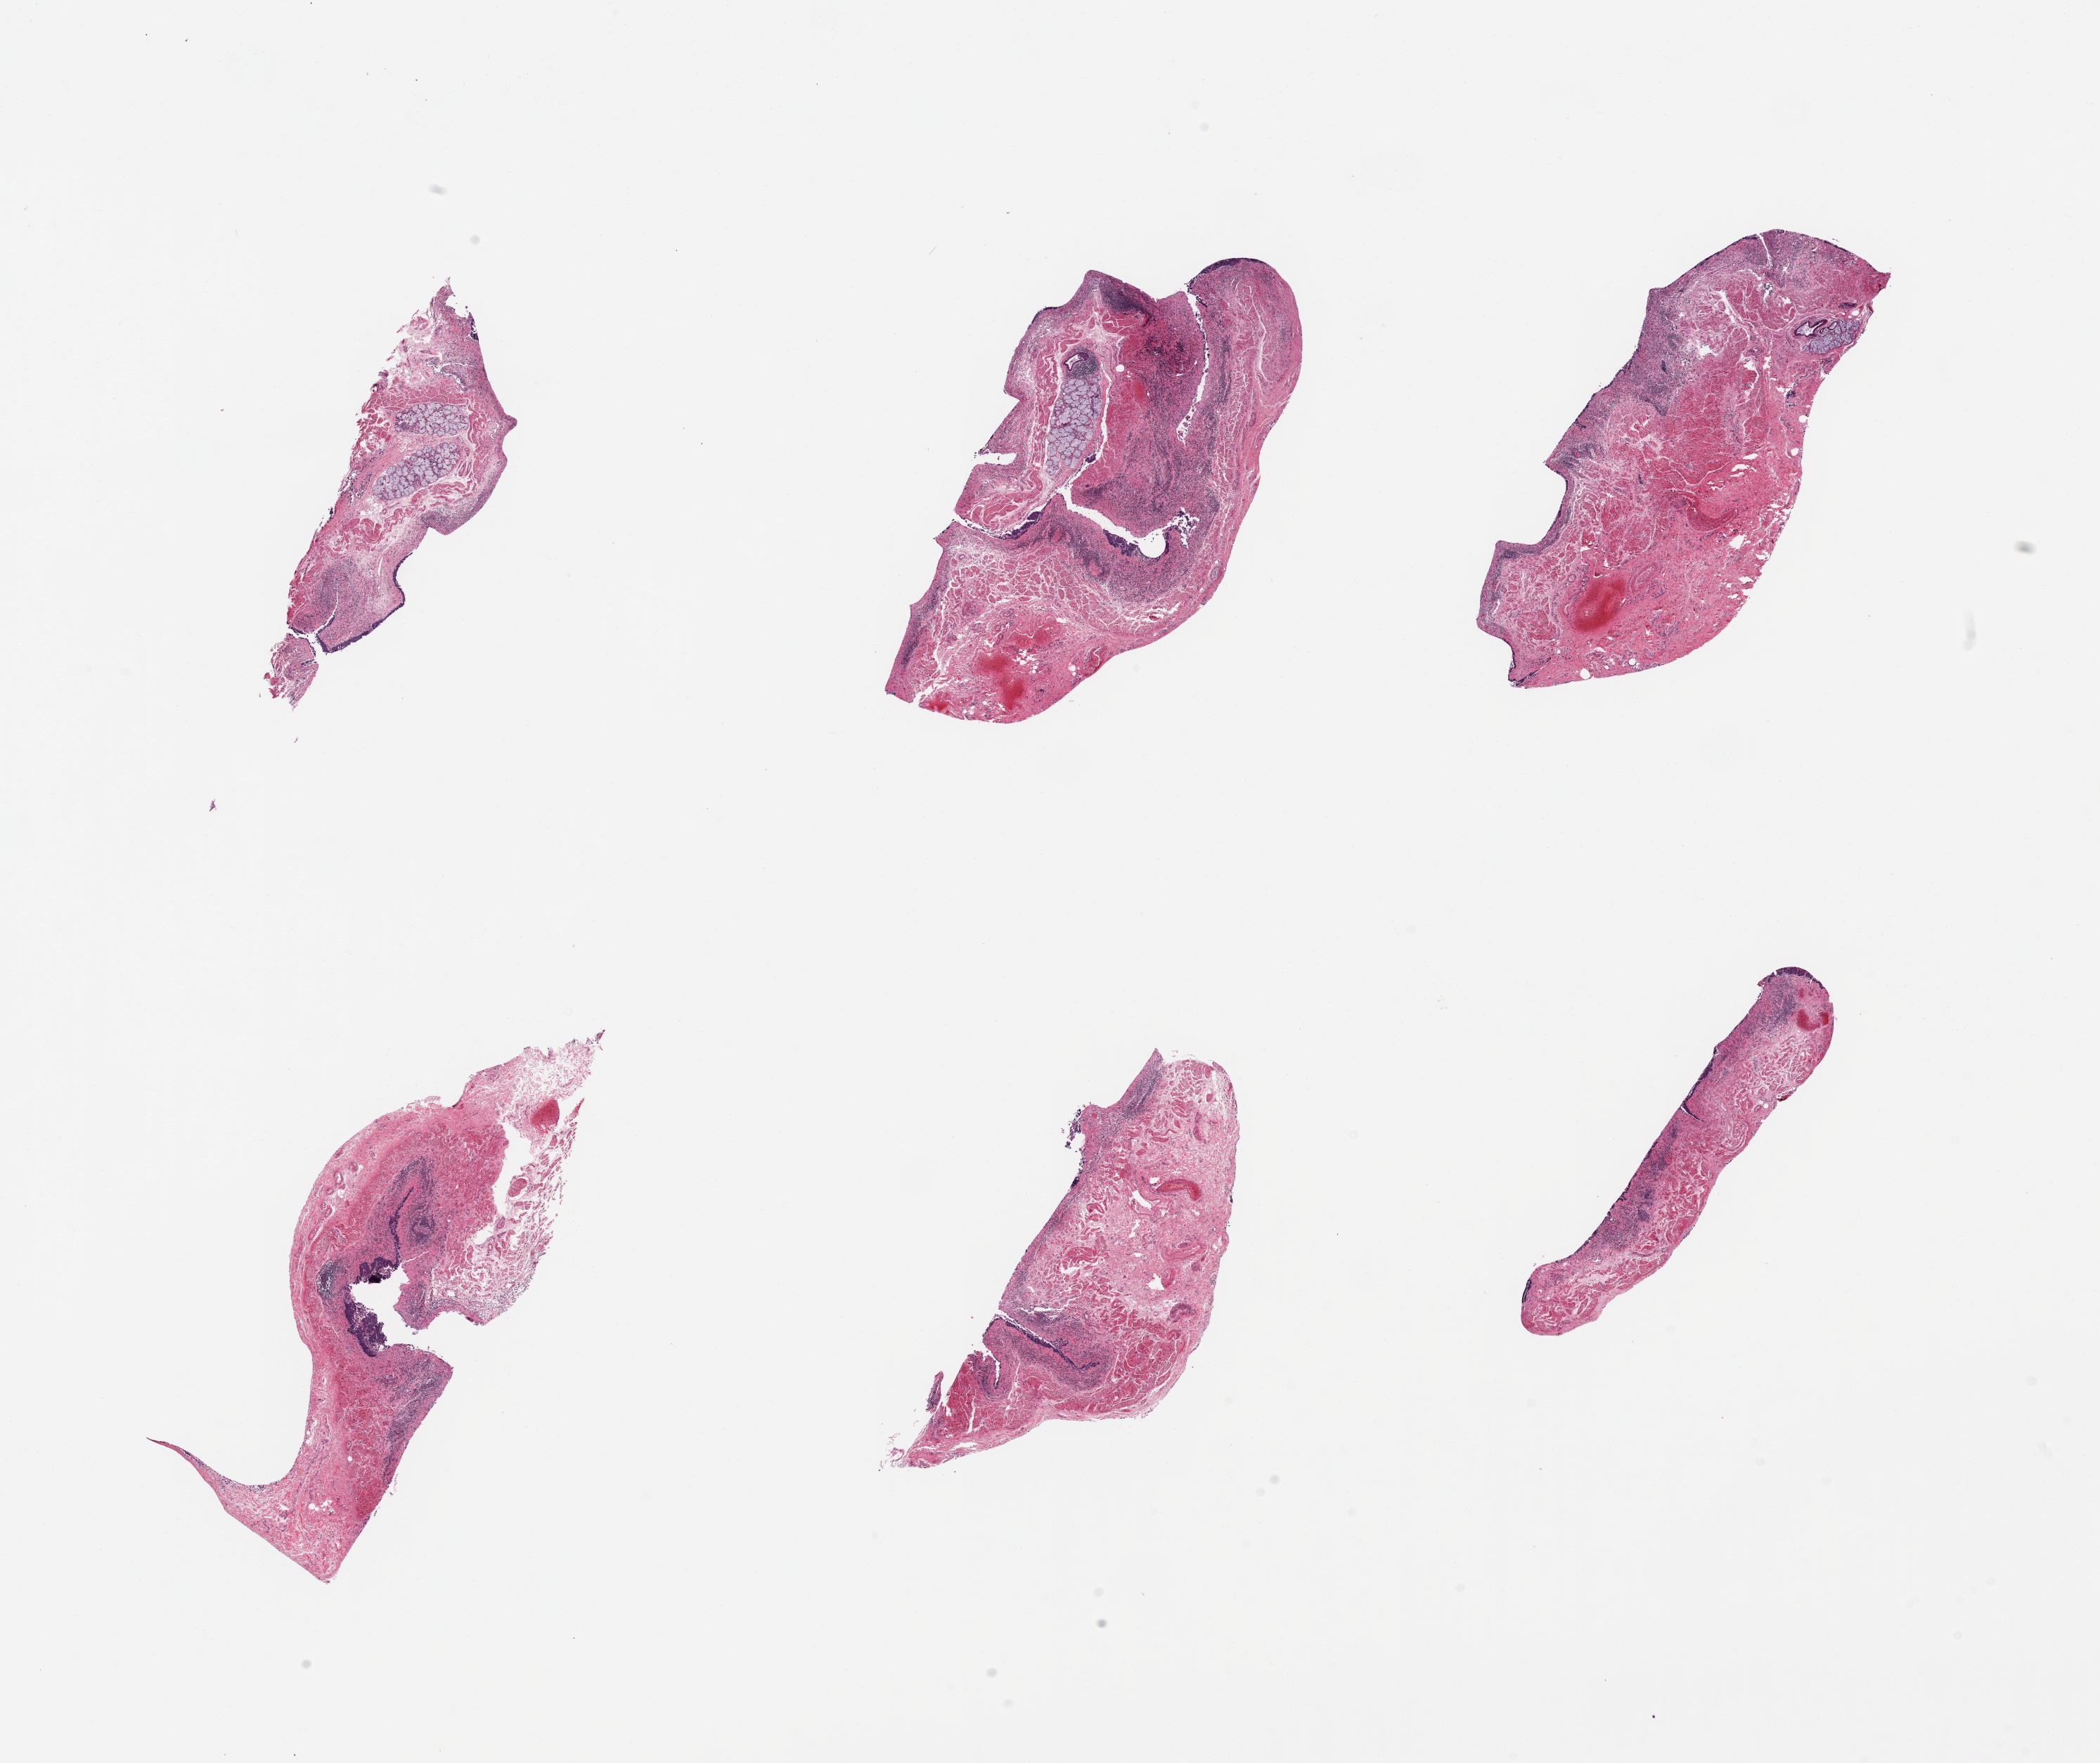
Haematoxylin and eosin whole-slide image, whole scanned area (about 23.6 x 19.8 mm, slide scanned at 20x) shown as a low-resolution overview, PAXgene-fixed paraffin-embedded (PFPE) section, sampled site (target tissue): esophageal mucous membrane, donor tissue sample. Male donor.
Pathologist's review note for this sample: 6 pieces; epithelium autolyzed and largely sloughed.